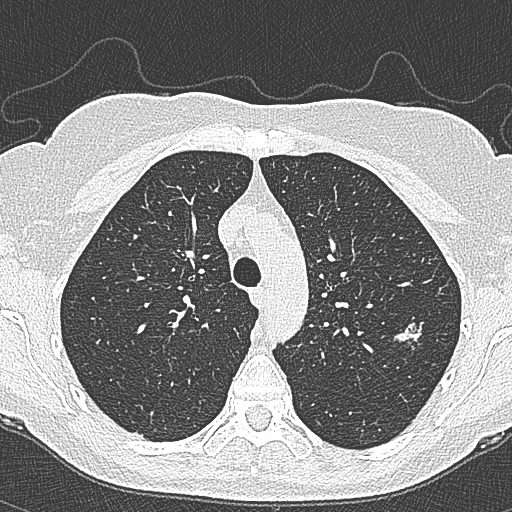
Chest CT (low-dose screening protocol), one axial image; second screening round (one year after baseline); lung window (W 1500 / L -600 HU); lung (sharp) reconstruction kernel (B80f); 120 kVp. Female, age 65 years at enrolment. Current smoker at enrolment.
Lesion marked by an expert reader, bounding box (x1, y1, x2, y2) in pixels: (394, 310, 441, 357). The screening reader recorded 4 non-calcified nodules or masses ≥4 mm on this exam; which of them this box marks is not recorded. Official screen result: positive, change unspecified: nodule(s) >= 4 mm or enlarging nodule(s), mass(es), or other non-specific abnormalities suspicious for lung cancer. Participant outcome: lung cancer diagnosed 54 days after this screen — bronchiolo-alveolar carcinoma, non-mucinous, left upper lobe, stage IA (AJCC 6th edition), 10 mm at pathology.